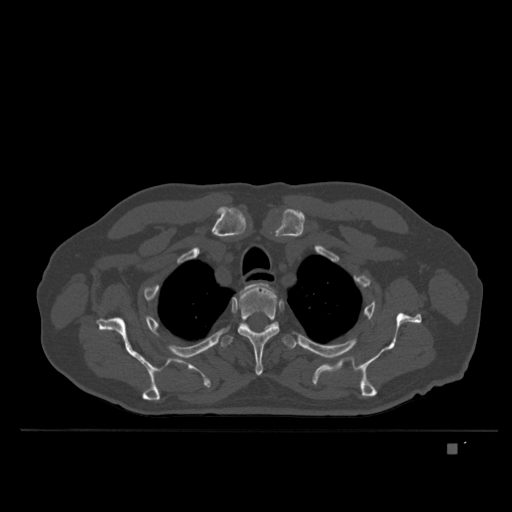
CT including the spine, one axial slice; slice 299 of 435 in the series (ordered by position); bone window (W 1800 / L 400 HU); 1.5 mm slice thickness; 512 × 512 image matrix. Patient: male, 73 years. From the clinical record (not read from this slice): primary cancer: skin.
Structures marked on this image (semi-automatic segmentation, software-assisted and operator-edited):
- T2 vertebra: box from (x=239, y=283) to (x=272, y=294) px
- T3 vertebra: (x=237, y=284)–(x=280, y=376)
- T4 vertebra: (x=219, y=335)–(x=299, y=350)